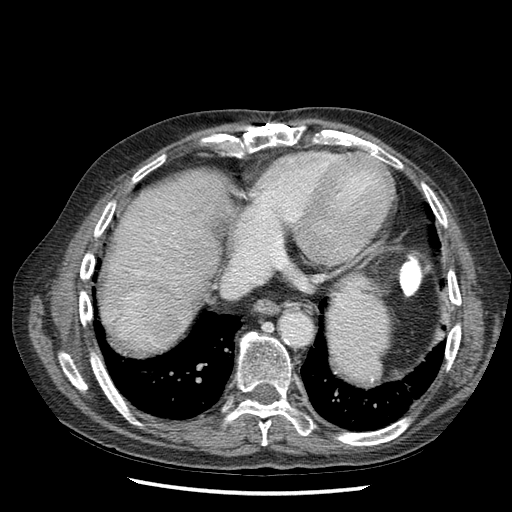
Contrast-enhanced abdominal CT (liver protocol), one axial slice; position 60 of 67 along the scan axis; reconstruction kernel STANDARD; 120 kVp; soft-tissue window (W 400 / L 40 HU); 512 × 512 image matrix, field of view 360 × 360 mm. From the clinical record (not read from this slice): diagnosis: hepatocellular carcinoma (patient treated with transarterial chemoembolisation; whether this scan precedes or follows treatment is not stated here); TNM stage (as recorded): Stage-I; Child-Pugh class: A; tumour nodularity: uninodular.
Outlined on this slice (semi-automatic segmentation, software-assisted and operator-edited):
- liver parenchyma outside the tumour (the mass and vessels are separate outlines, so this box may not span the whole liver): bounding box [x1, y1, x2, y2] px = [108, 172, 228, 342]
- mass: [118, 291, 182, 341]
- liver vessels: [146, 338, 150, 341]